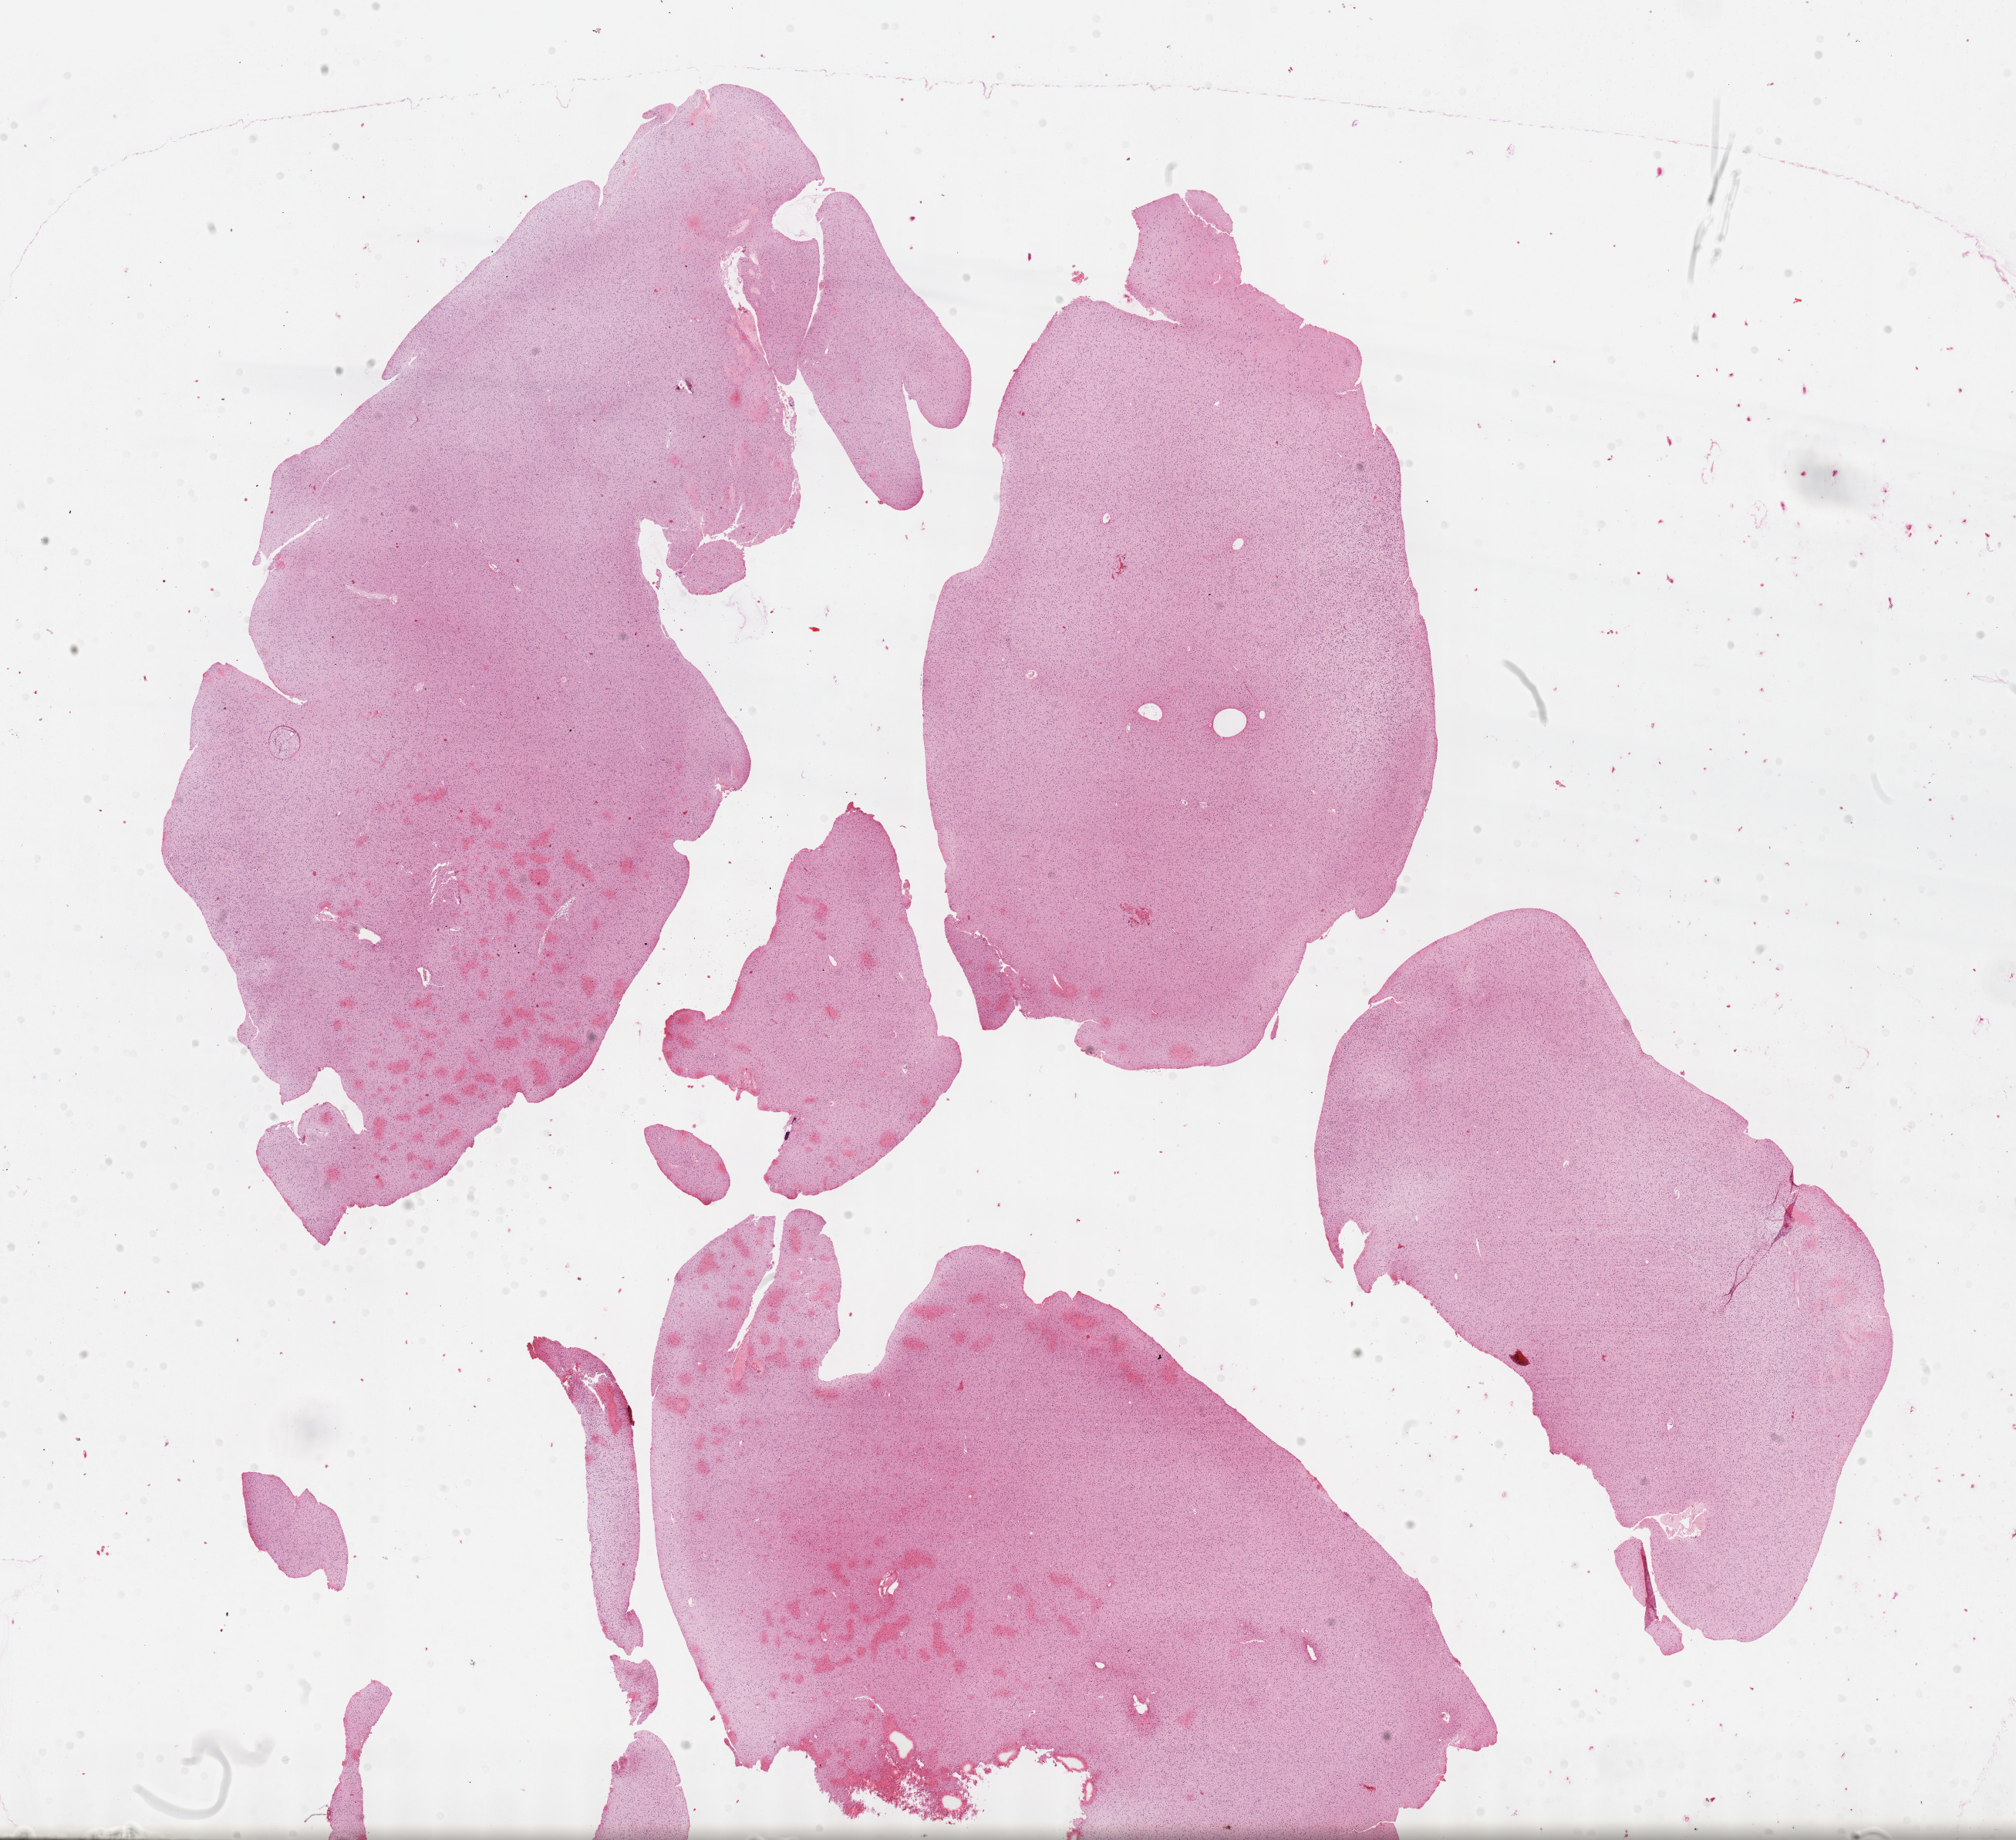
Digitized Hematoxylin and eosin (H&E) stained tissue section (whole slide), shown as a low-resolution overview of the whole scanned area (about 21.1 x 19.3 mm, slide scanned at 40x), formalin-fixed paraffin-embedded (FFPE) diagnostic section, sample: primary tumour, brain. Female patient; age at initial diagnosis 23 years. Histologic grade: G2 (moderately differentiated).
Laterality: left. Diagnosis: Mixed glioma (cerebrum).